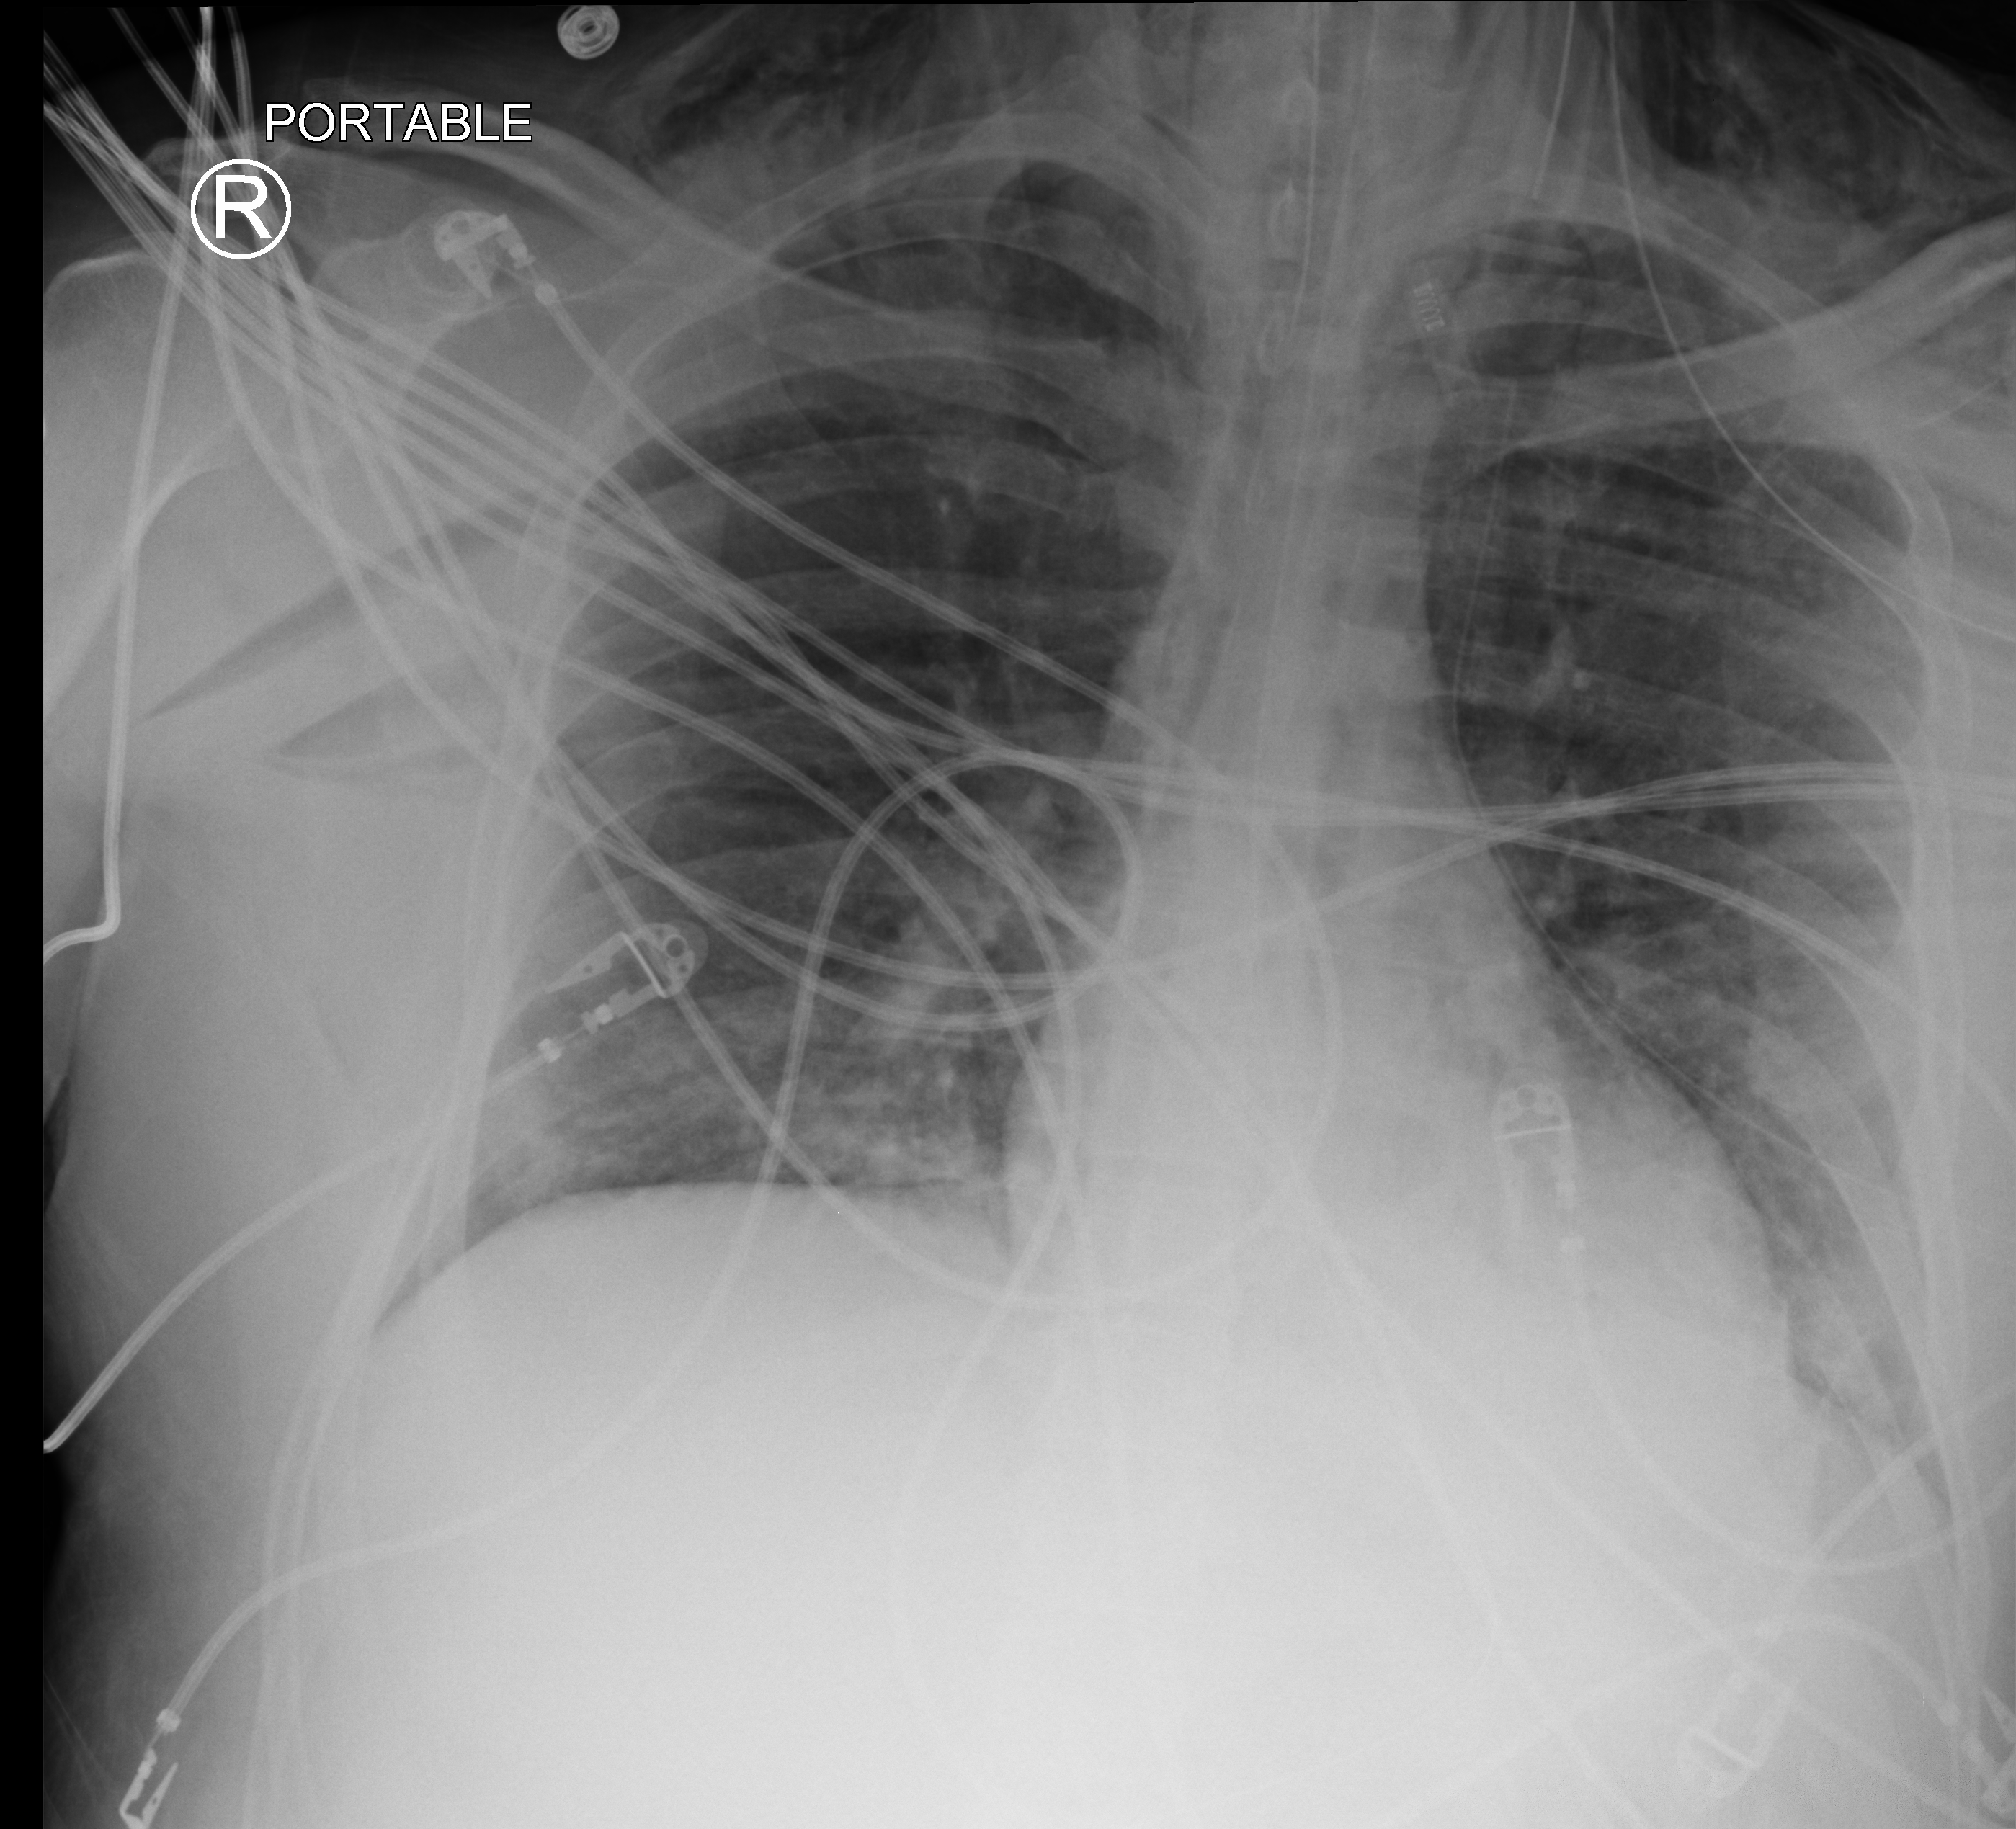
Chest X-ray (portable). Male patient hospitalised with COVID-19, age 18–59 years.
From the hospital-stay record, not from the radiograph (when in the stay this image was taken is not recorded): COPD (admission record): no; other chronic lung disease (admission record): no; hypertension (admission record): no.